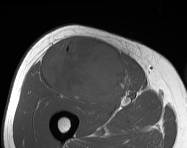
MRI of an extremity soft-tissue mass, one axial slice. Position 81 of 114 along the scan axis. MR volume resampled by the dataset authors to the PET/CT grid (not the native acquisition matrix). 3.27 mm slice thickness. 187 × 148 image matrix, field of view 183 × 145 mm. Male patient. From the clinical record (not read from this slice): histological type: pleiomorphic leiomyosarcoma; grade: intermediate; site of the primary tumour: right thigh.
Structures marked on this image (expert contour drawn on MRI and transferred to this co-registered scan by the dataset authors):
- gross tumour volume including surrounding oedema: bounding box (x1, y1, x2, y2) in pixels: (43, 38, 131, 101)
- gross tumour volume (mass): (43, 38, 131, 101)